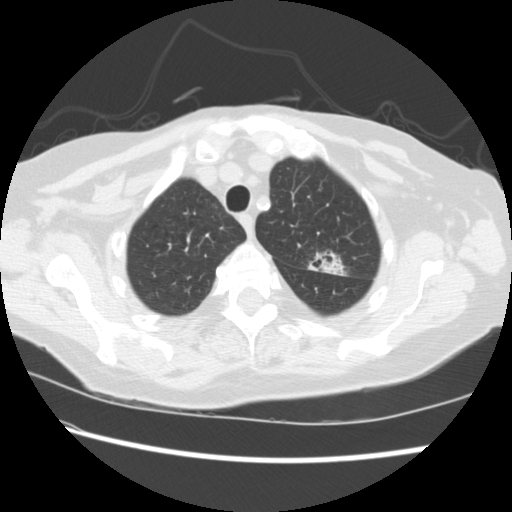
Low-dose screening chest CT, one axial slice. Position 181 of 224 along the scan axis. Reconstruction kernel STANDARD. Lung window (W 1500 / L -600 HU). 2.5 mm slice thickness. 512 × 512 image matrix, field of view 340 × 340 mm.
Outlined on this slice (expert manual segmentation):
- lesion 1 (tumor, upper lobe of left lung): bounding box <318,260,345,276> (left, top, right, bottom; pixels)